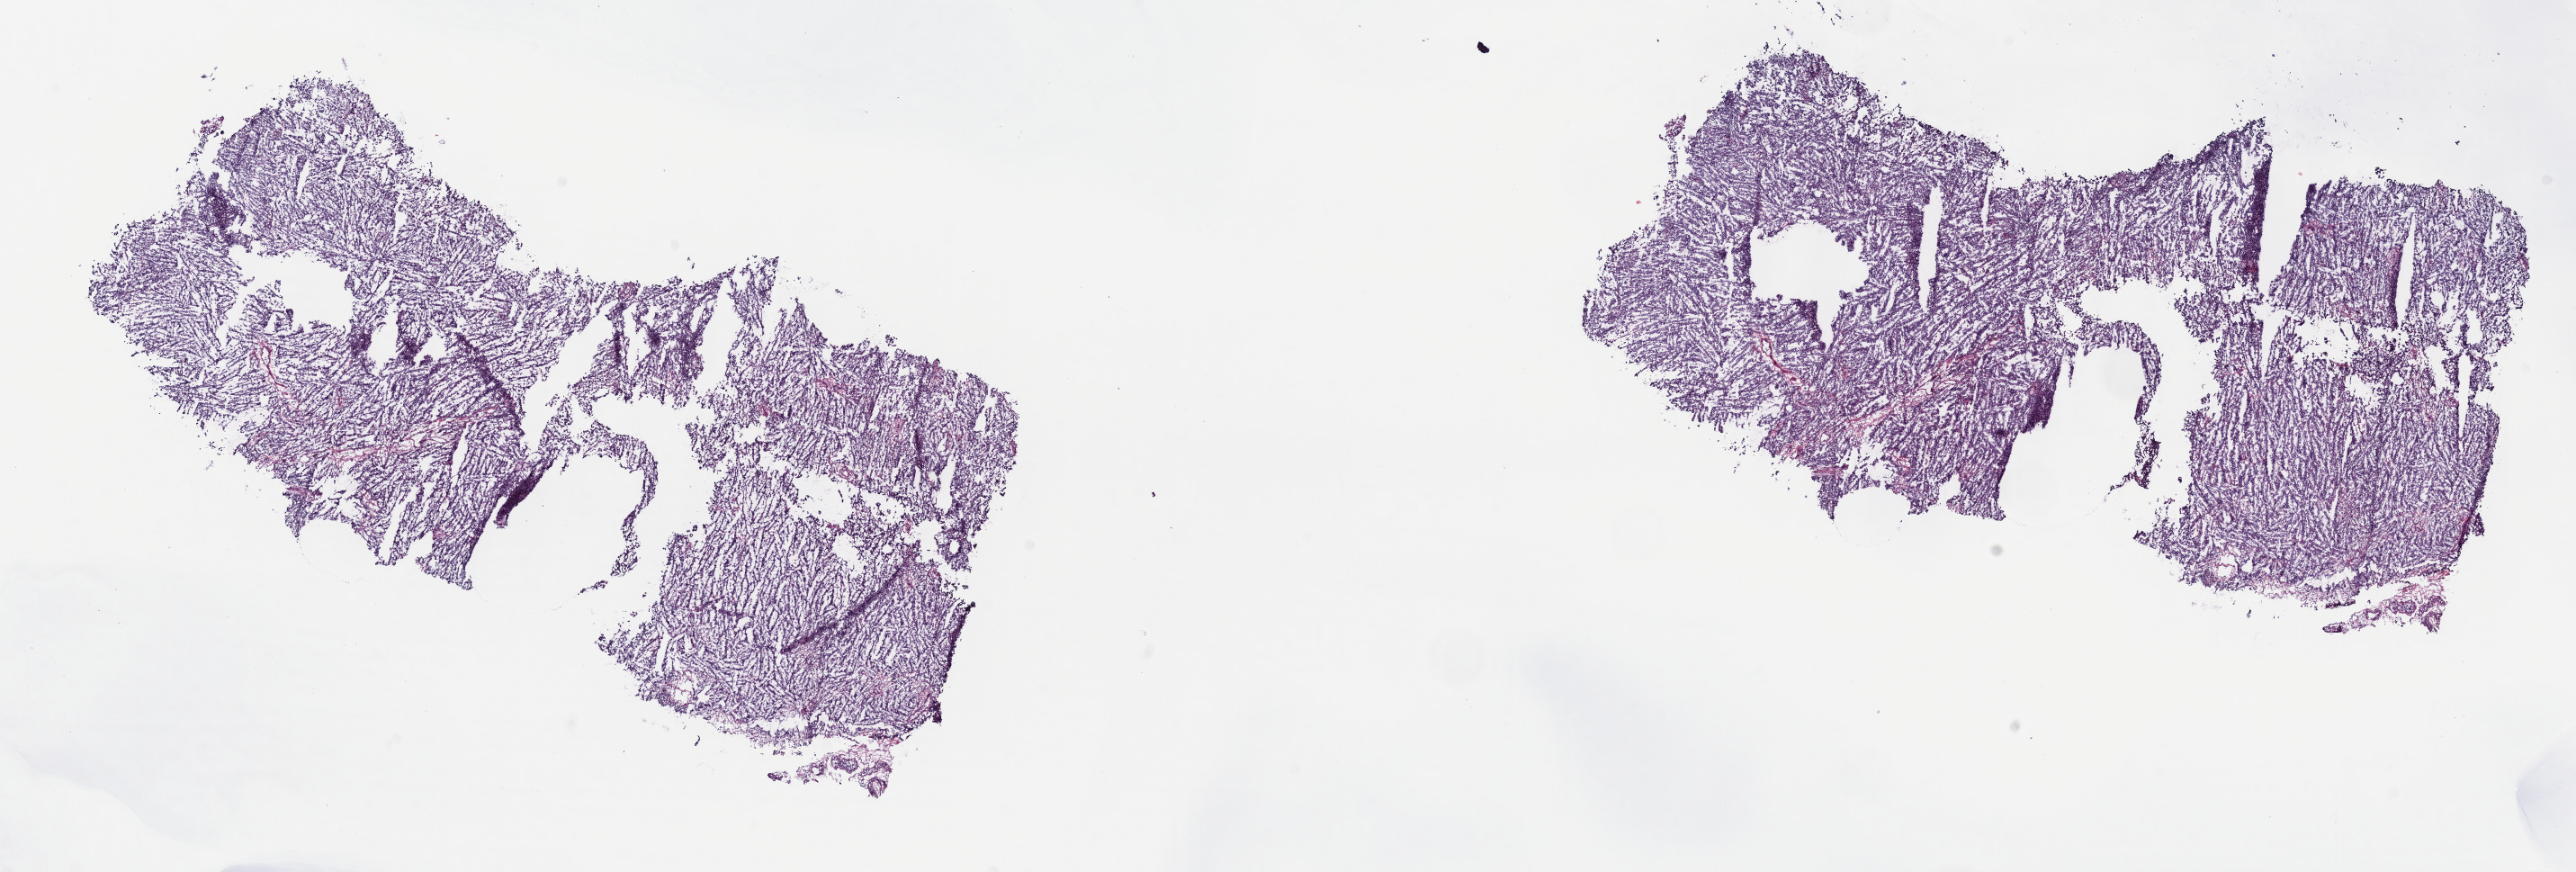
Whole-slide histology image, Hematoxylin and eosin (H&E) stained, whole scanned area (about 23.2 x 7.8 mm, slide scanned at 40x) shown as a low-resolution overview; frozen section from the top of the tissue portion; sample: primary tumour, testis. Patient: male, age at initial diagnosis 26 years. Slide review estimates, as recorded: tumour cells 90%, tumour nuclei 90%, normal cells 0%, stromal cells 10%, necrosis 0%. Inflammatory infiltration, as recorded: lymphocyte infiltration 40%, monocyte infiltration 20%, neutrophil infiltration 20%.
TNM: T2 N0 M0. Histologic diagnosis: Seminoma, NOS. AJCC pathologic stage: I. Laterality: left.